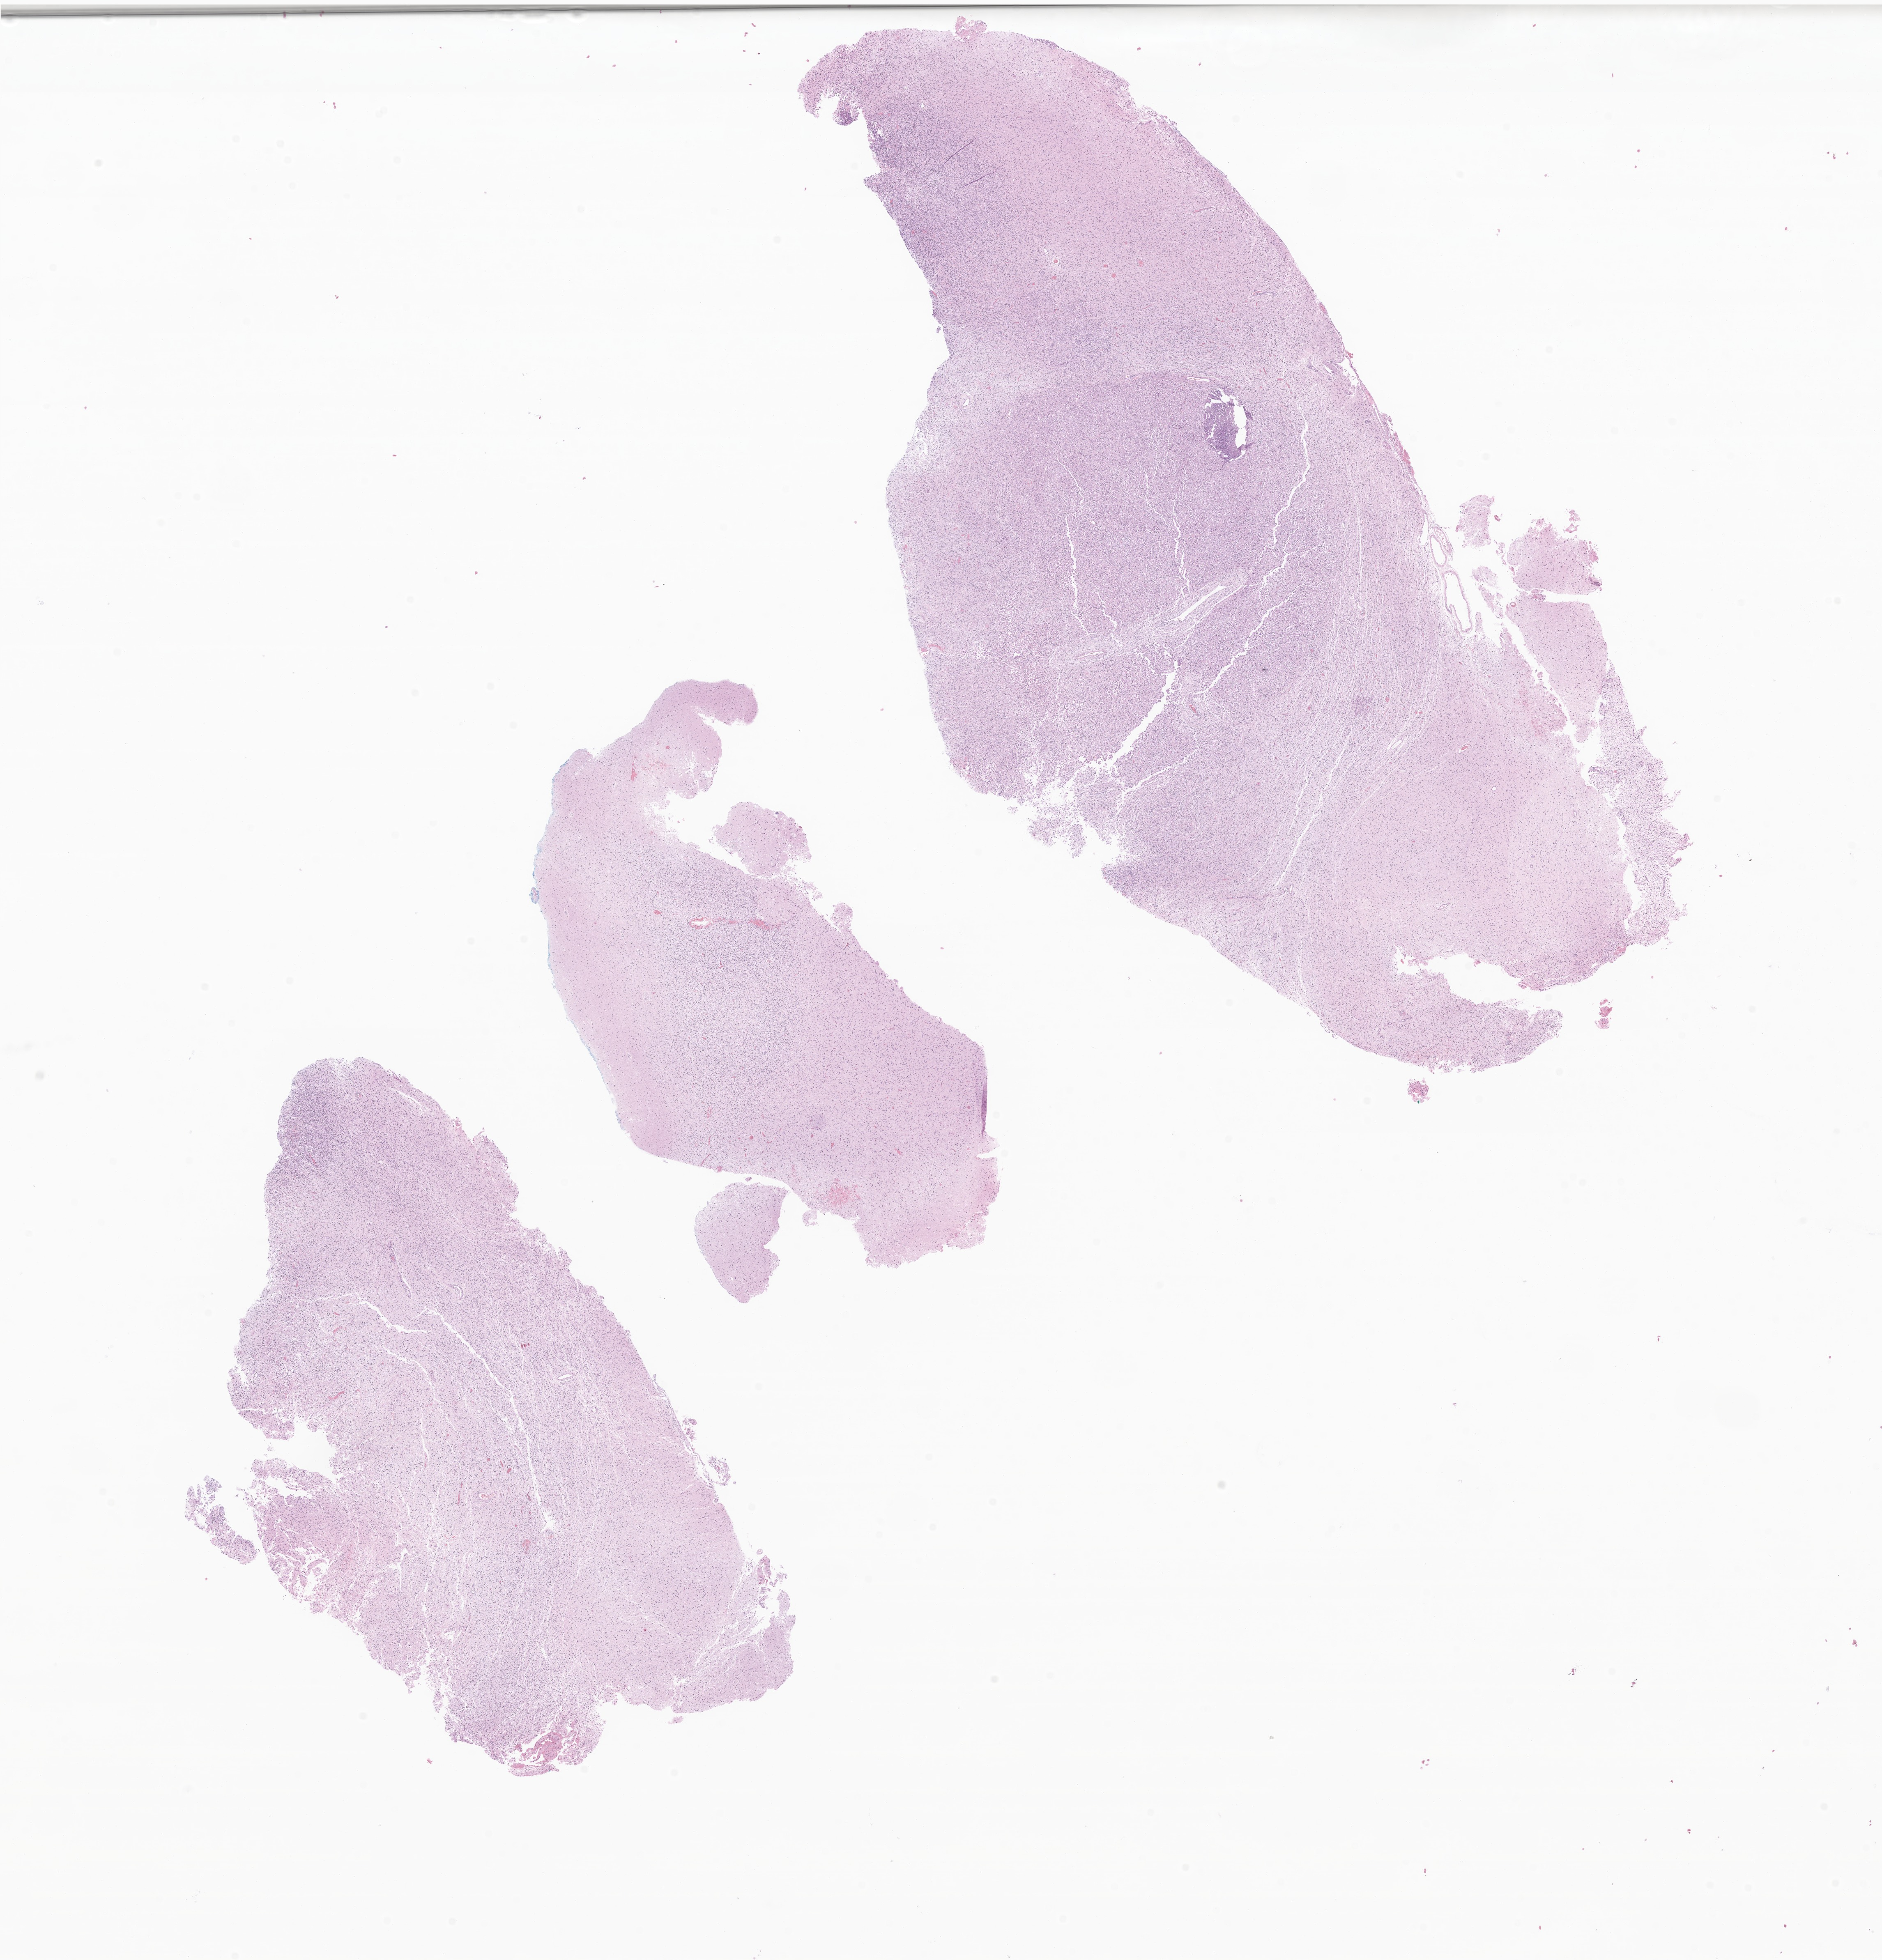
Digitized hematoxylin and eosin (H&E)-stained section of tumor tissue from the brain, low-resolution overview of the scanned area, about 19.3 x 20.1 mm, formalin-fixed paraffin-embedded section. Patient male; age 174 months (14 years 6 months).
- recorded diagnosis: Neoplasm, malignant